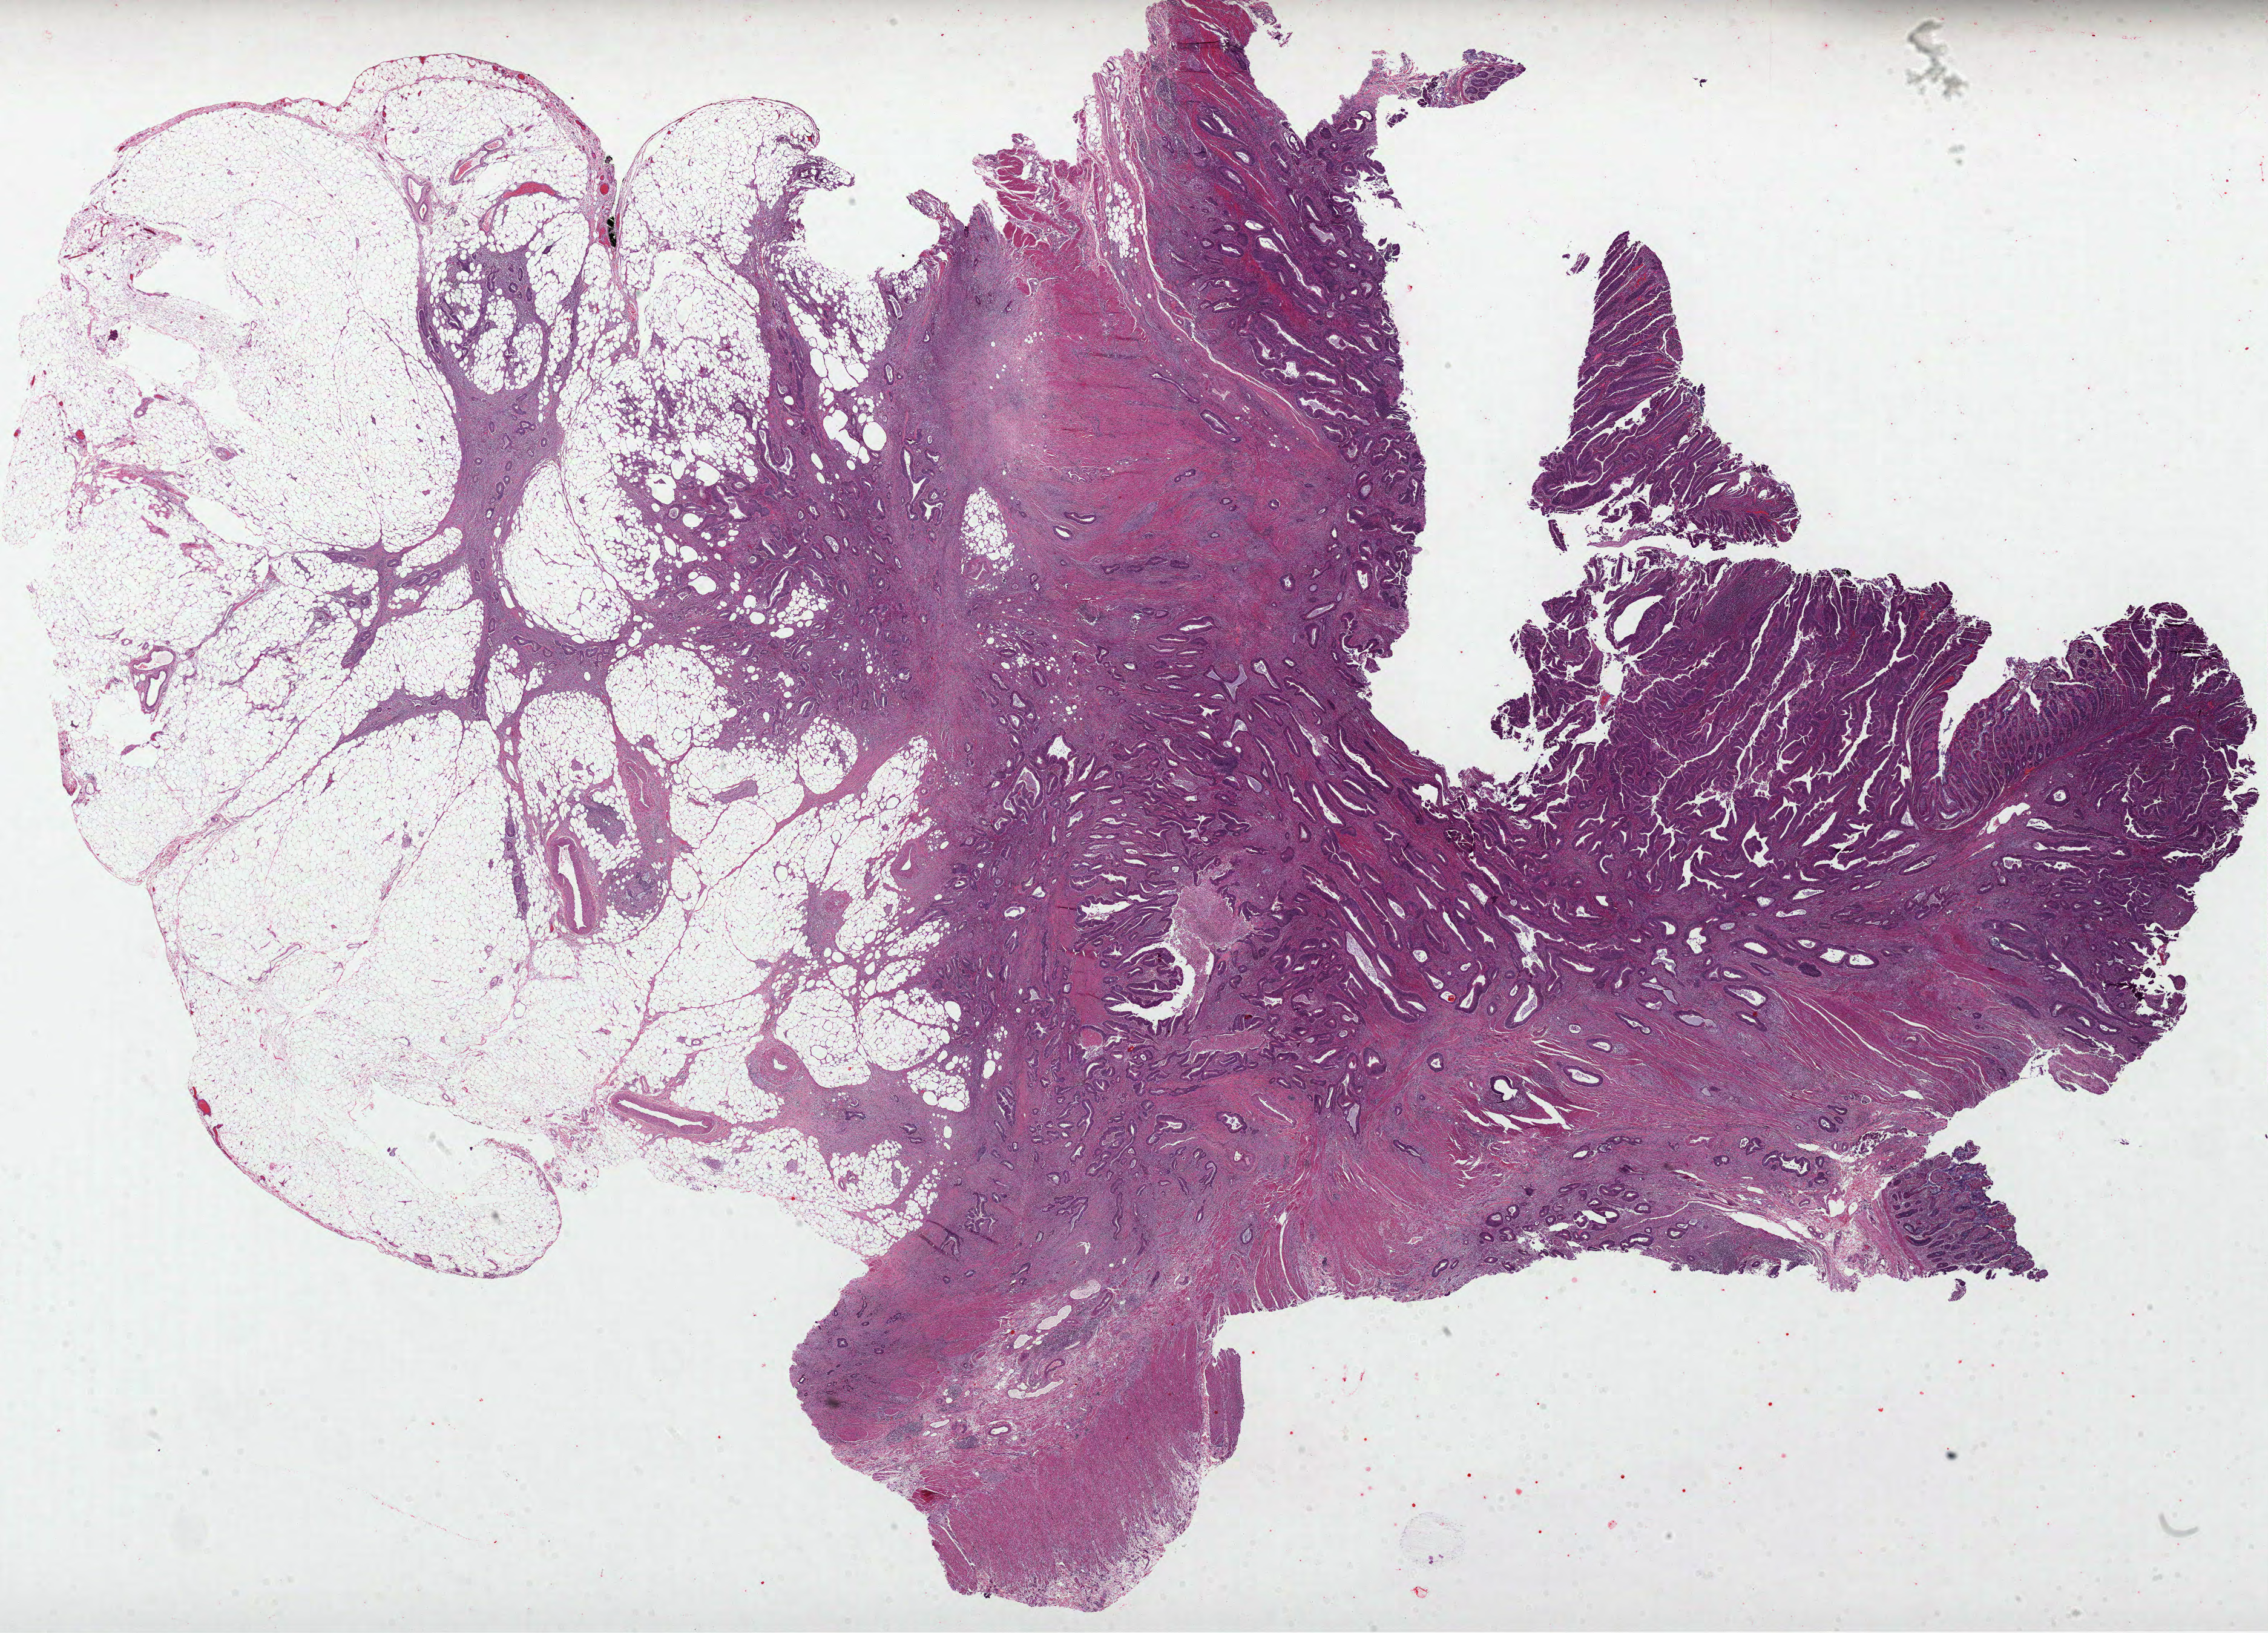
Hematoxylin and eosin (H&E) stained whole-slide image, whole scanned area (about 30.2 x 21.8 mm) shown as a low-resolution overview. Formalin-fixed paraffin-embedded (FFPE) diagnostic section. Sample: primary tumour, colon. Patient: male, age at initial diagnosis 47 years.
Diagnosis: Adenocarcinoma, NOS (cecum).